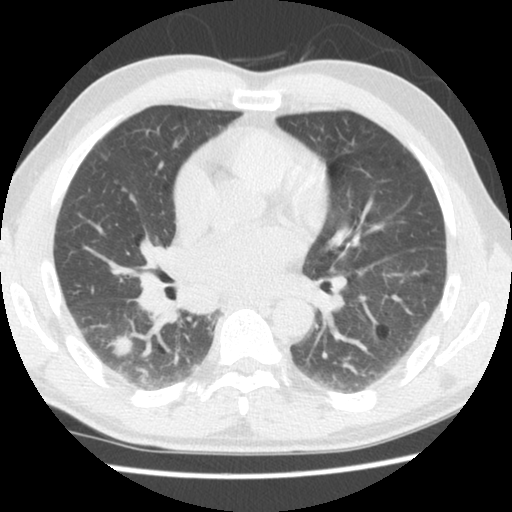
Low-dose screening chest CT, axial slice, second annual screen, lung window (W 1500 / L -600 HU), 140 kVp. Male, age 60 years at enrolment. Former smoker at enrolment.
• Lesion marked by an expert reader, bounding box (x1, y1, x2, y2) in pixels: (91, 322, 143, 372).
• The exam's reader record, not a measurement of the box and not confirmed to be the same lesion: non-calcified nodule or mass ≥4 mm, right lower lobe, 17 × 15 mm, poorly defined margins, soft tissue attenuation, pre-existing on the prior screen: yes; interval growth: yes.
• Official screen result: positive, other.
• Lung cancer was diagnosed 44 days after this screen: adenocarcinoma, NOS, right lower lobe, stage IA (AJCC 6th edition), 18 mm at pathology.